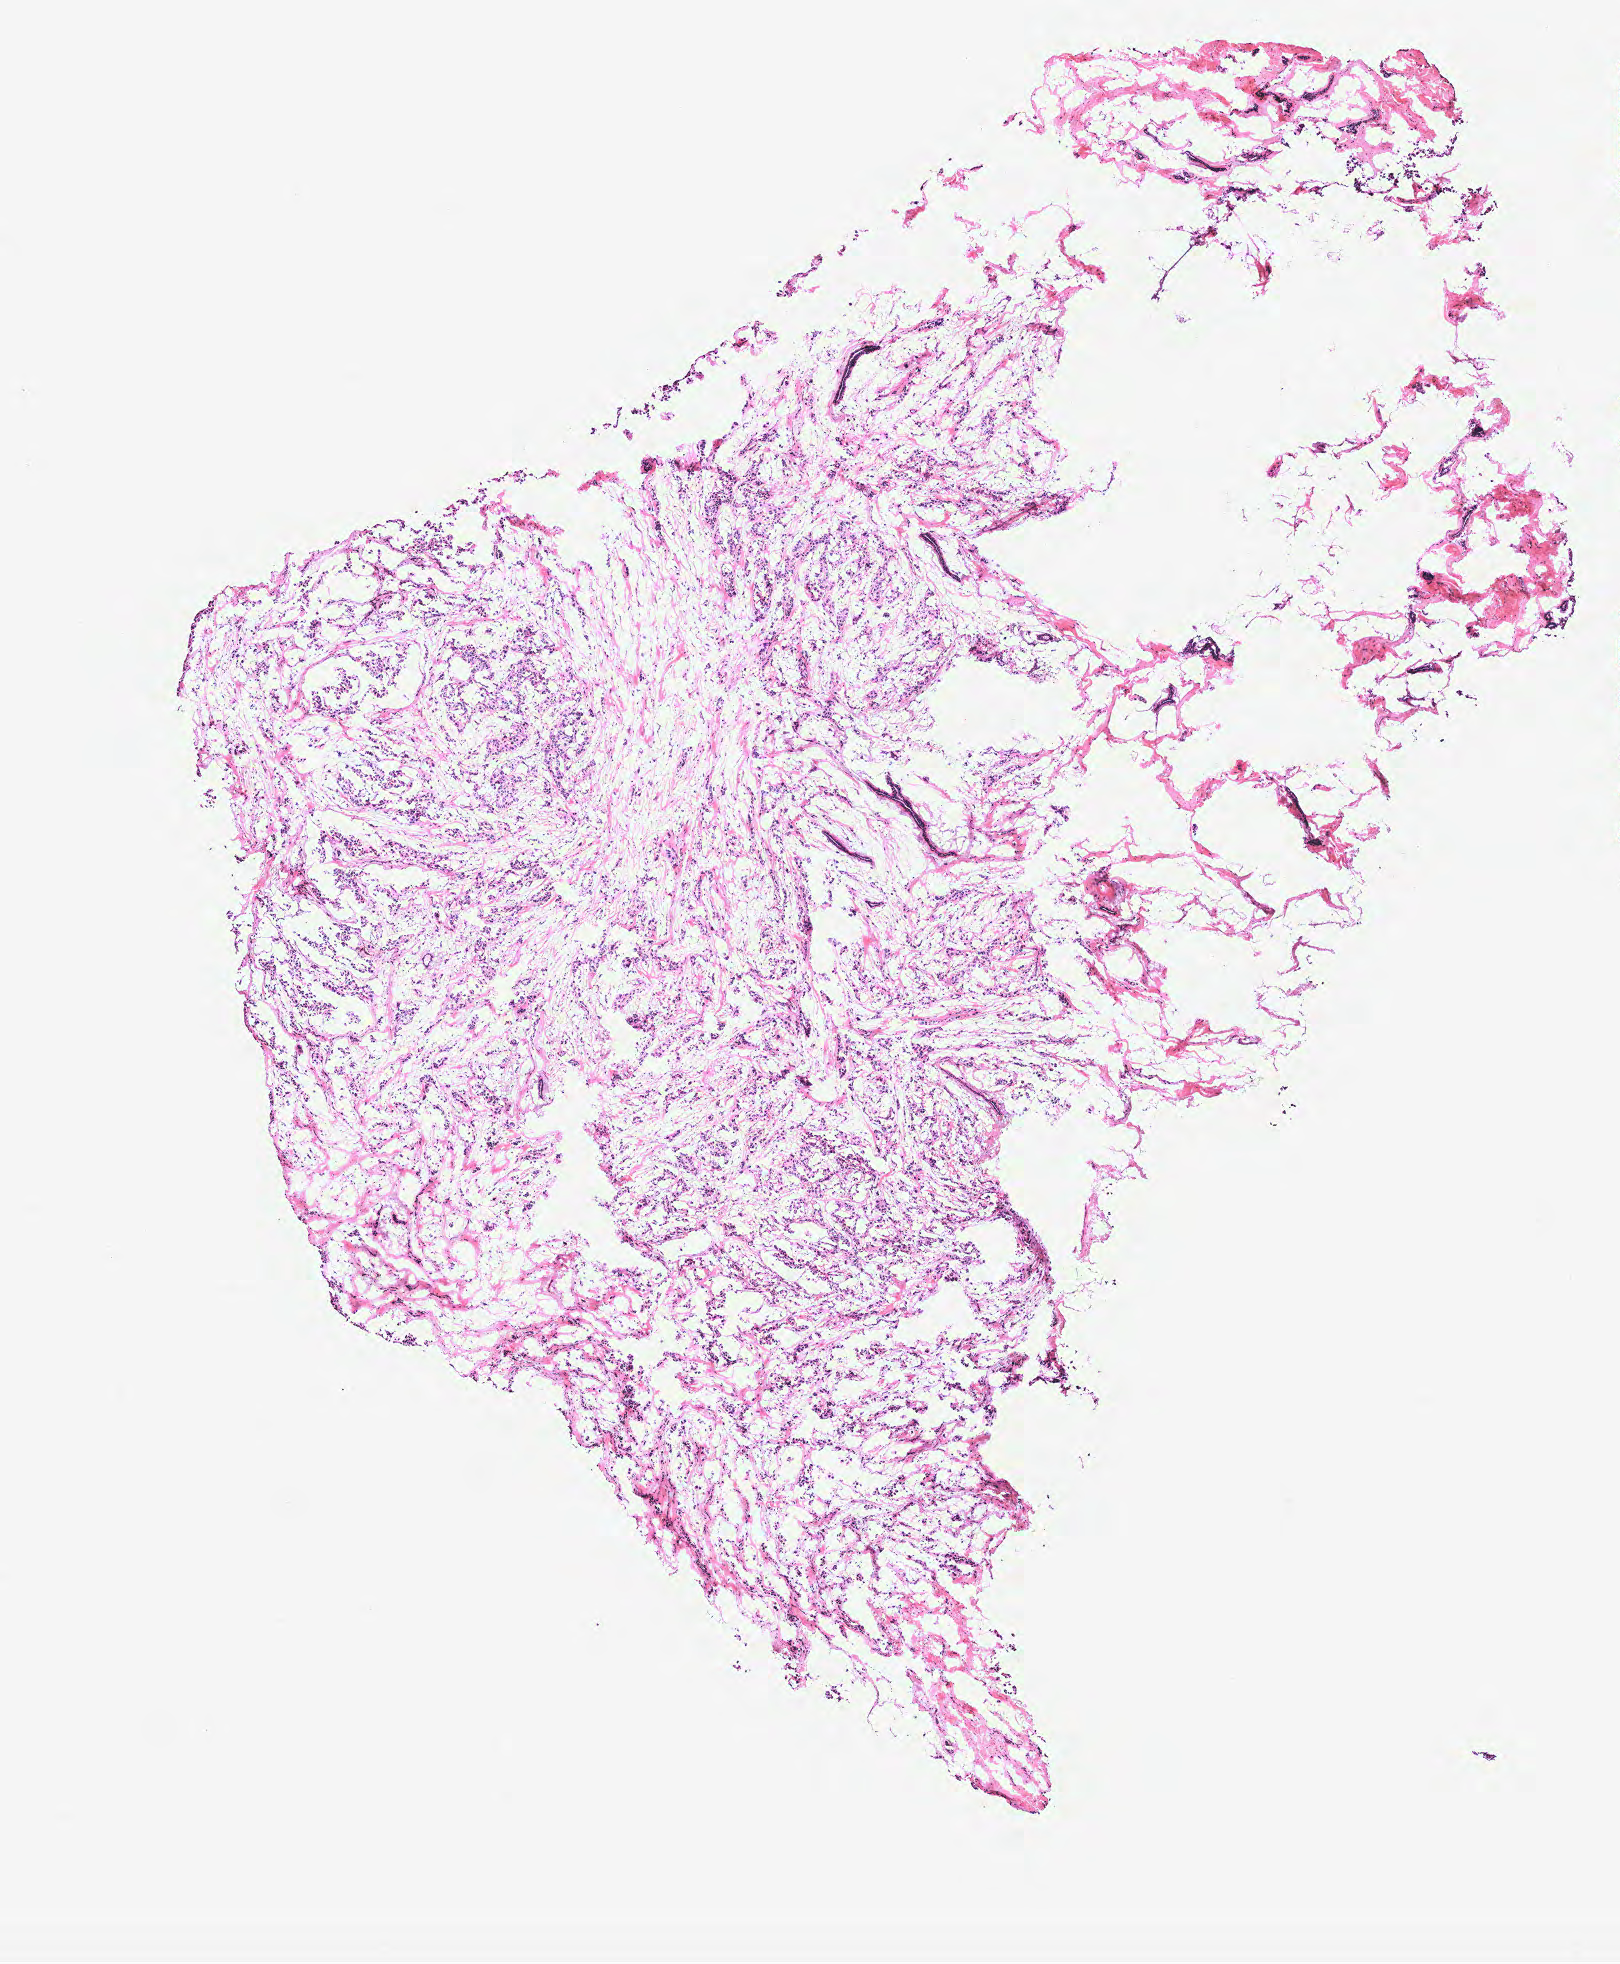
H&E-stained whole-slide image — whole scanned area (about 6.5 x 7.9 mm) shown as a low-resolution overview. Tumour tissue sample, breast. 71-year-old female patient.
Diagnosis: Infiltrating duct carcinoma, NOS.